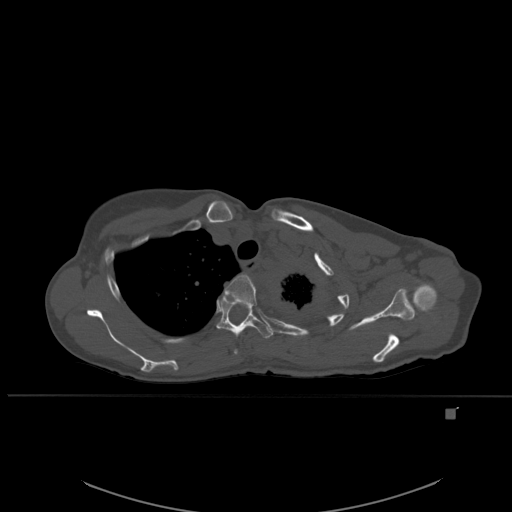
CT including the spine, one axial slice. Position 417 of 537 along the scan axis. Bone window (W 1800 / L 400 HU). 1.5 mm slice thickness. 512 × 512 image matrix, field of view 440 × 440 mm. Female patient, age 45 years. Case-level facts recorded for this patient, not image findings: primary cancer: lung.
Outlined on this slice (semi-automatically segmented with operator editing):
- T3 vertebra: bounding box (x1, y1, x2, y2) in pixels: (224, 274, 257, 354)
- T4 vertebra: (217, 294, 273, 339)